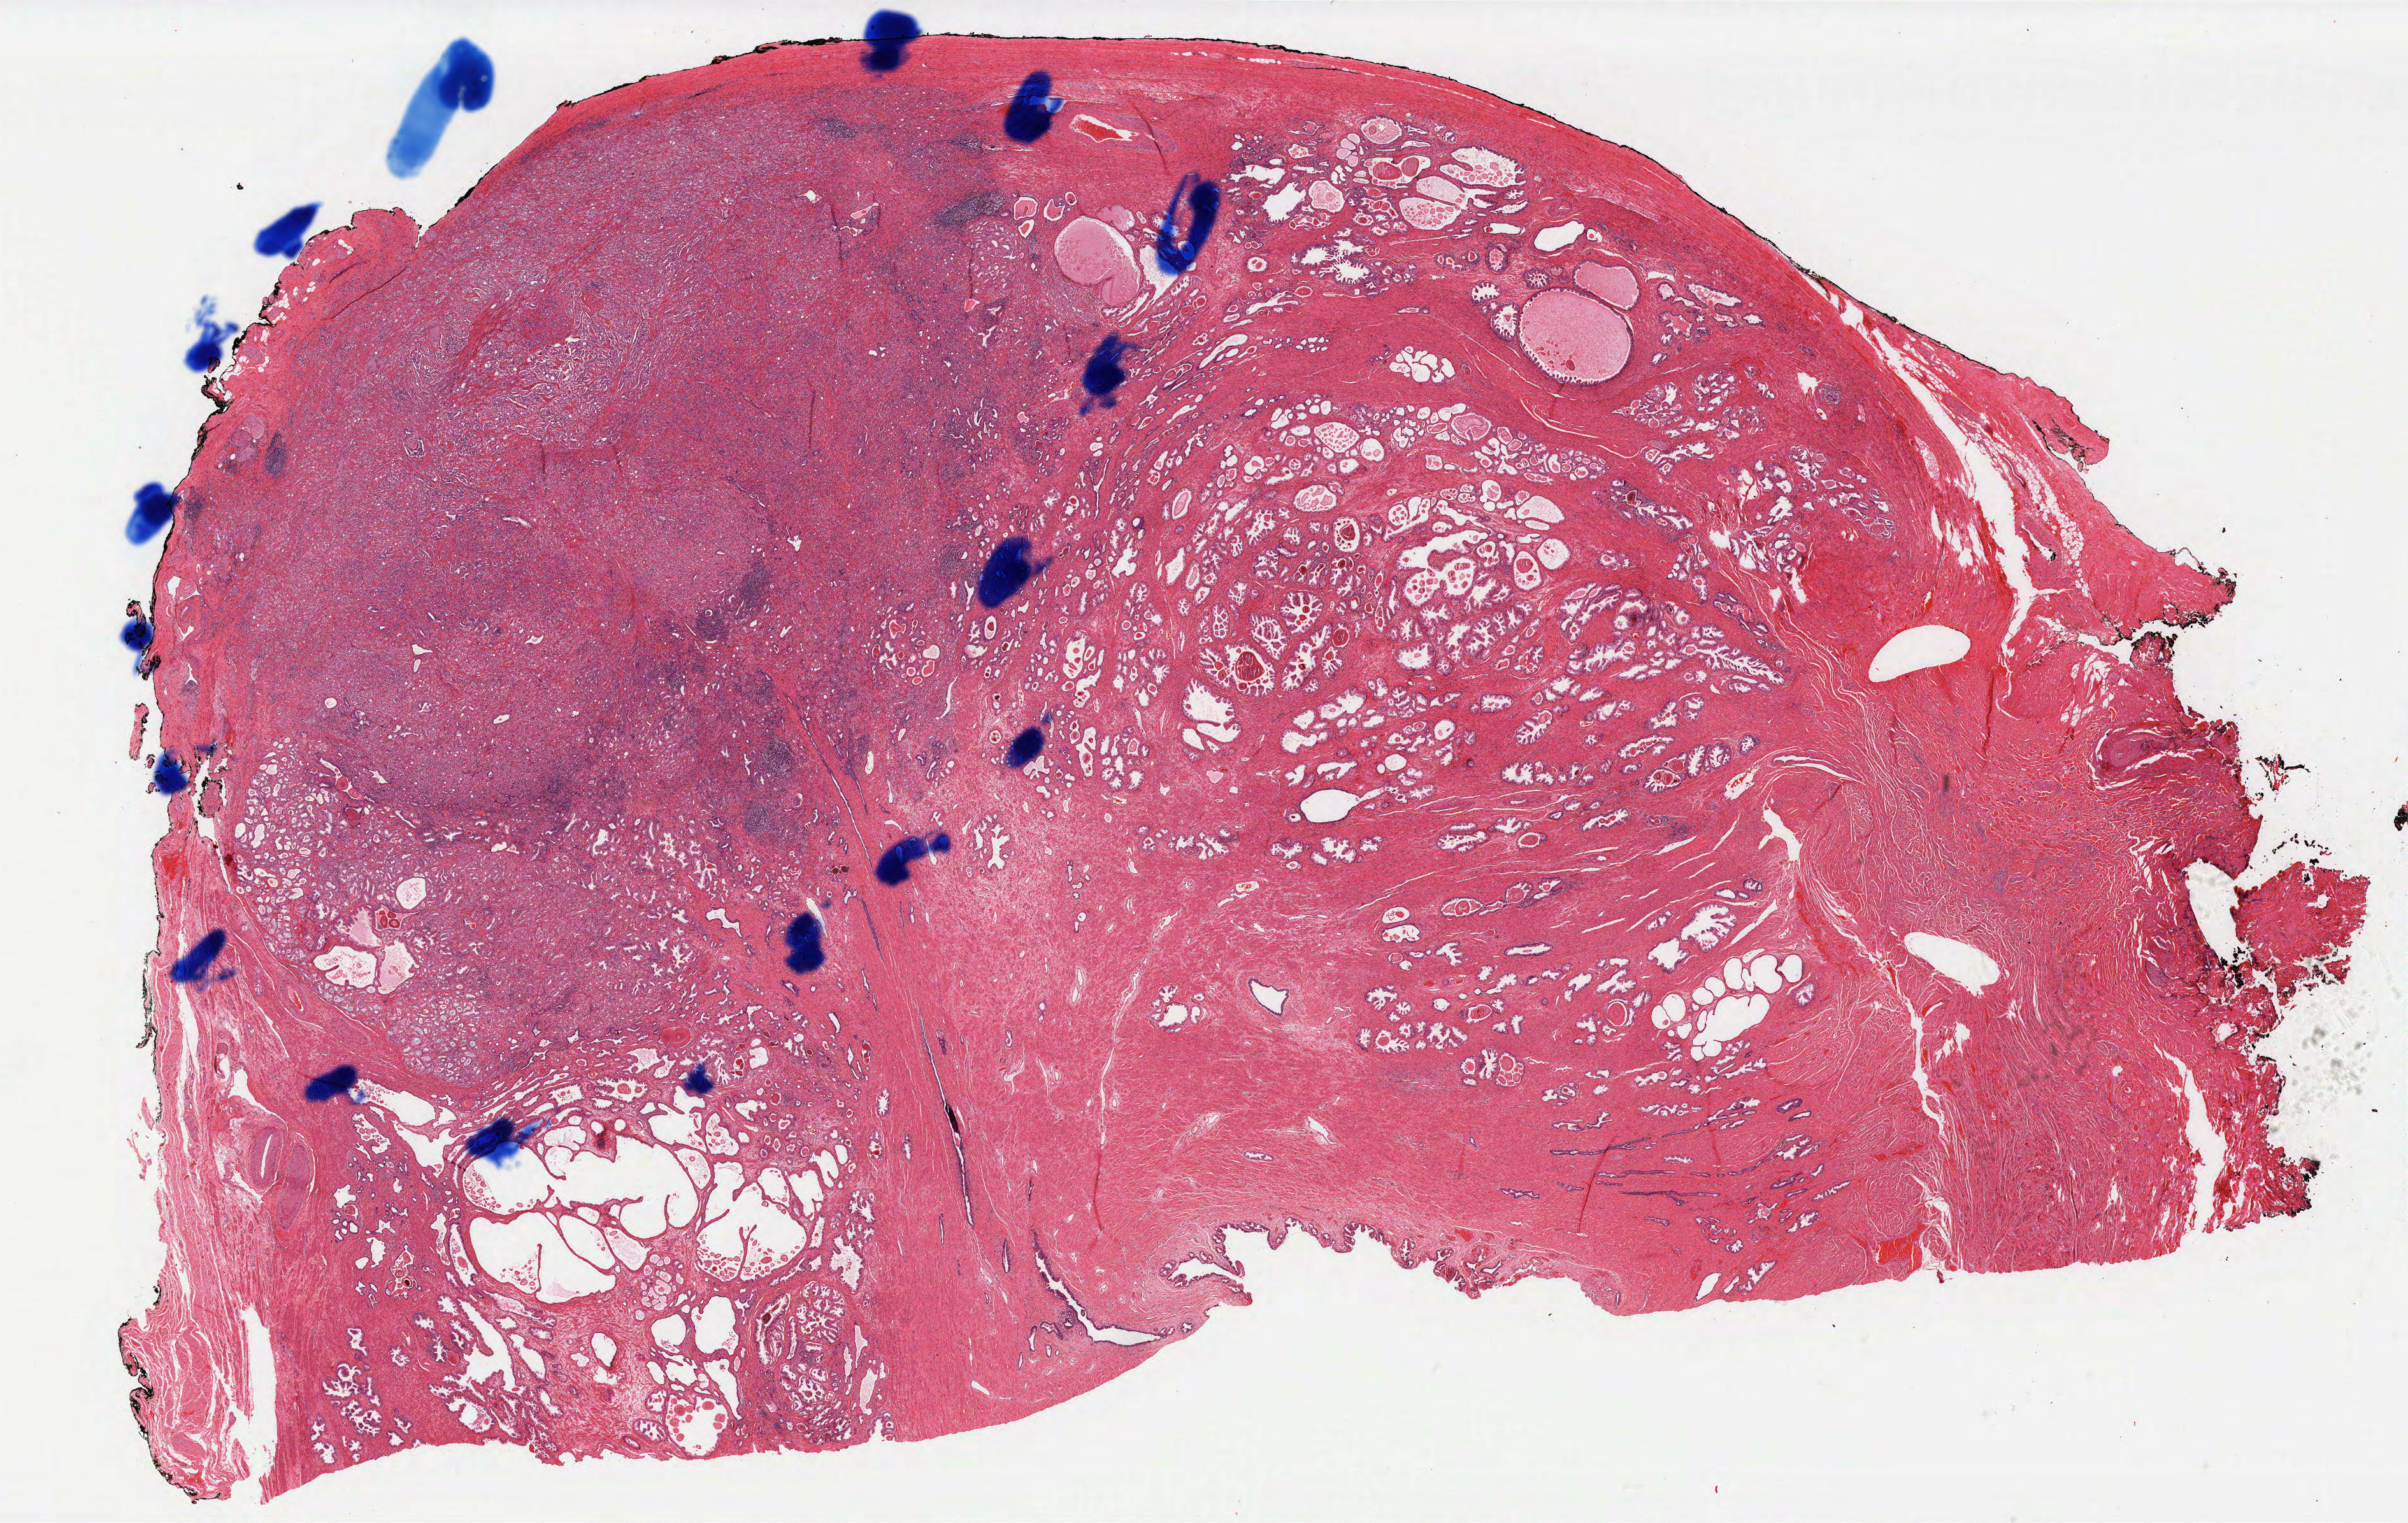
Digitized H&E-stained tissue section (whole slide) — whole scanned area (about 30.3 x 19.1 mm, from a 40x scan) shown as a low-resolution overview. FFPE section. Prostate, primary tumour sample. Male, age 67 years at initial diagnosis. Gleason score: 7 (4+3).
* histologic diagnosis: Adenocarcinoma, NOS
* lymph nodes positive (case pathology): 0 of 12 examined